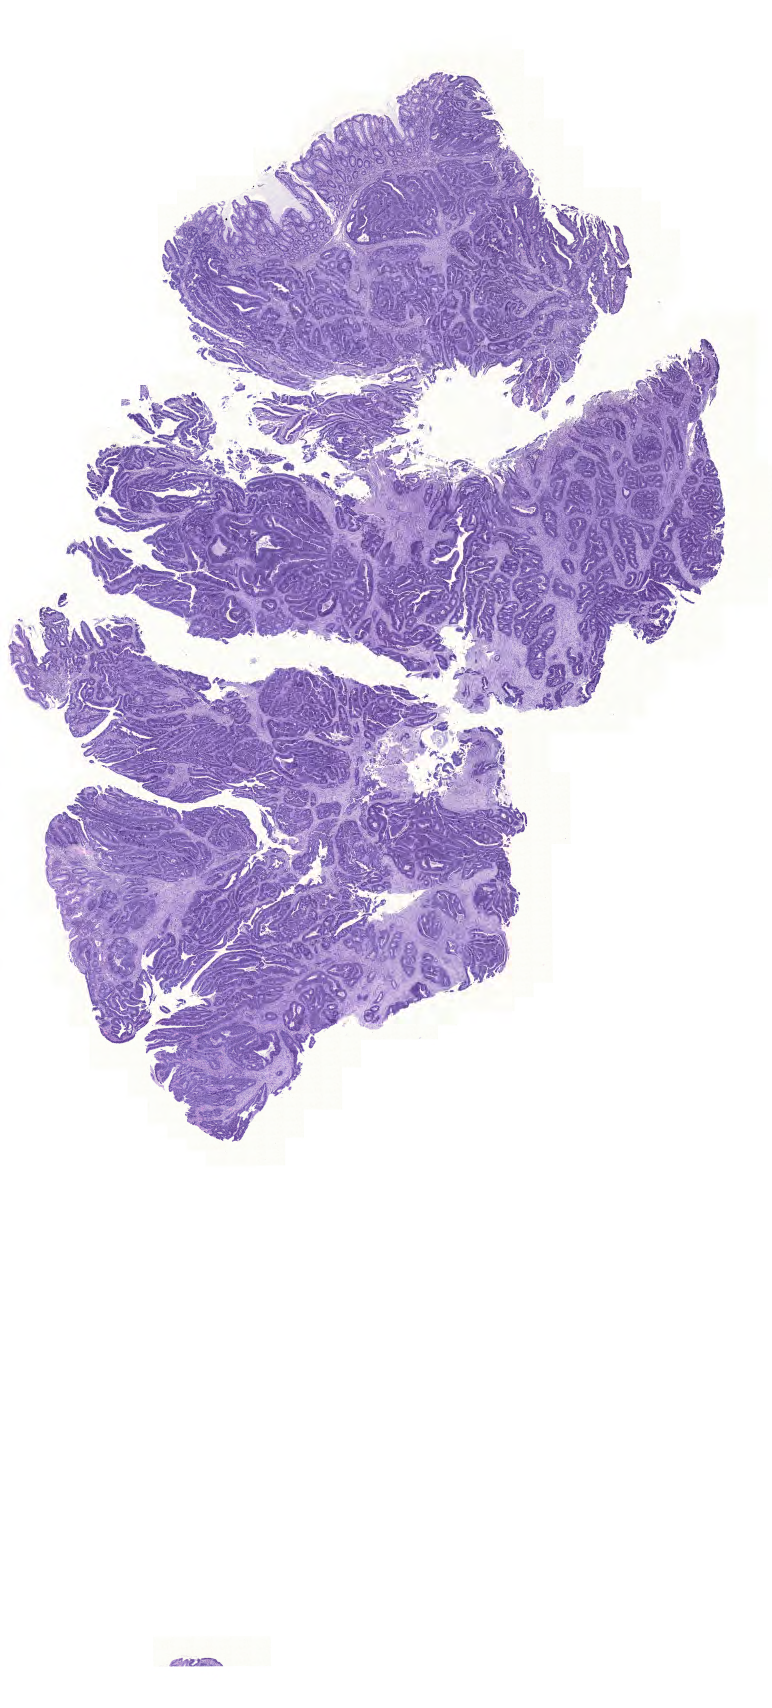
H&E-stained whole-slide image, low-resolution overview of the scanned area, about 11.5 x 25.4 mm (slide scanned at 20x), formalin-fixed paraffin-embedded (FFPE) diagnostic section, colon, primary tumour sample. Male patient; age at initial diagnosis 87 years.
AJCC pathologic stage: II (5th edition). Diagnosis: Adenocarcinoma, NOS (sigmoid colon). Lymph nodes positive (case pathology): 0 of 22 examined.